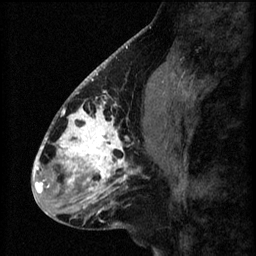
Breast MRI (dynamic contrast-enhanced), one sagittal slice; position 26 of 60 along the scan axis; 3 images stored at this slice position (order not interpretable as contrast timing); 1.5 T; TE 4.2 ms, TR 8.2 ms; 2.2 mm slice thickness; 256 × 256 image matrix. Female patient, age 41 years.
Annotated regions visible in this slice (semi-automatically segmented with operator editing):
- analysis volume of interest (the breast-tissue region the enhancement analysis was run in; not a lesion): bounding box (x1, y1, x2, y2) in pixels: (56, 104, 157, 207)
- tumour enhancement mask (voxels above the 70 % enhancement threshold inside the analysis volume of interest): (56, 104, 136, 207)